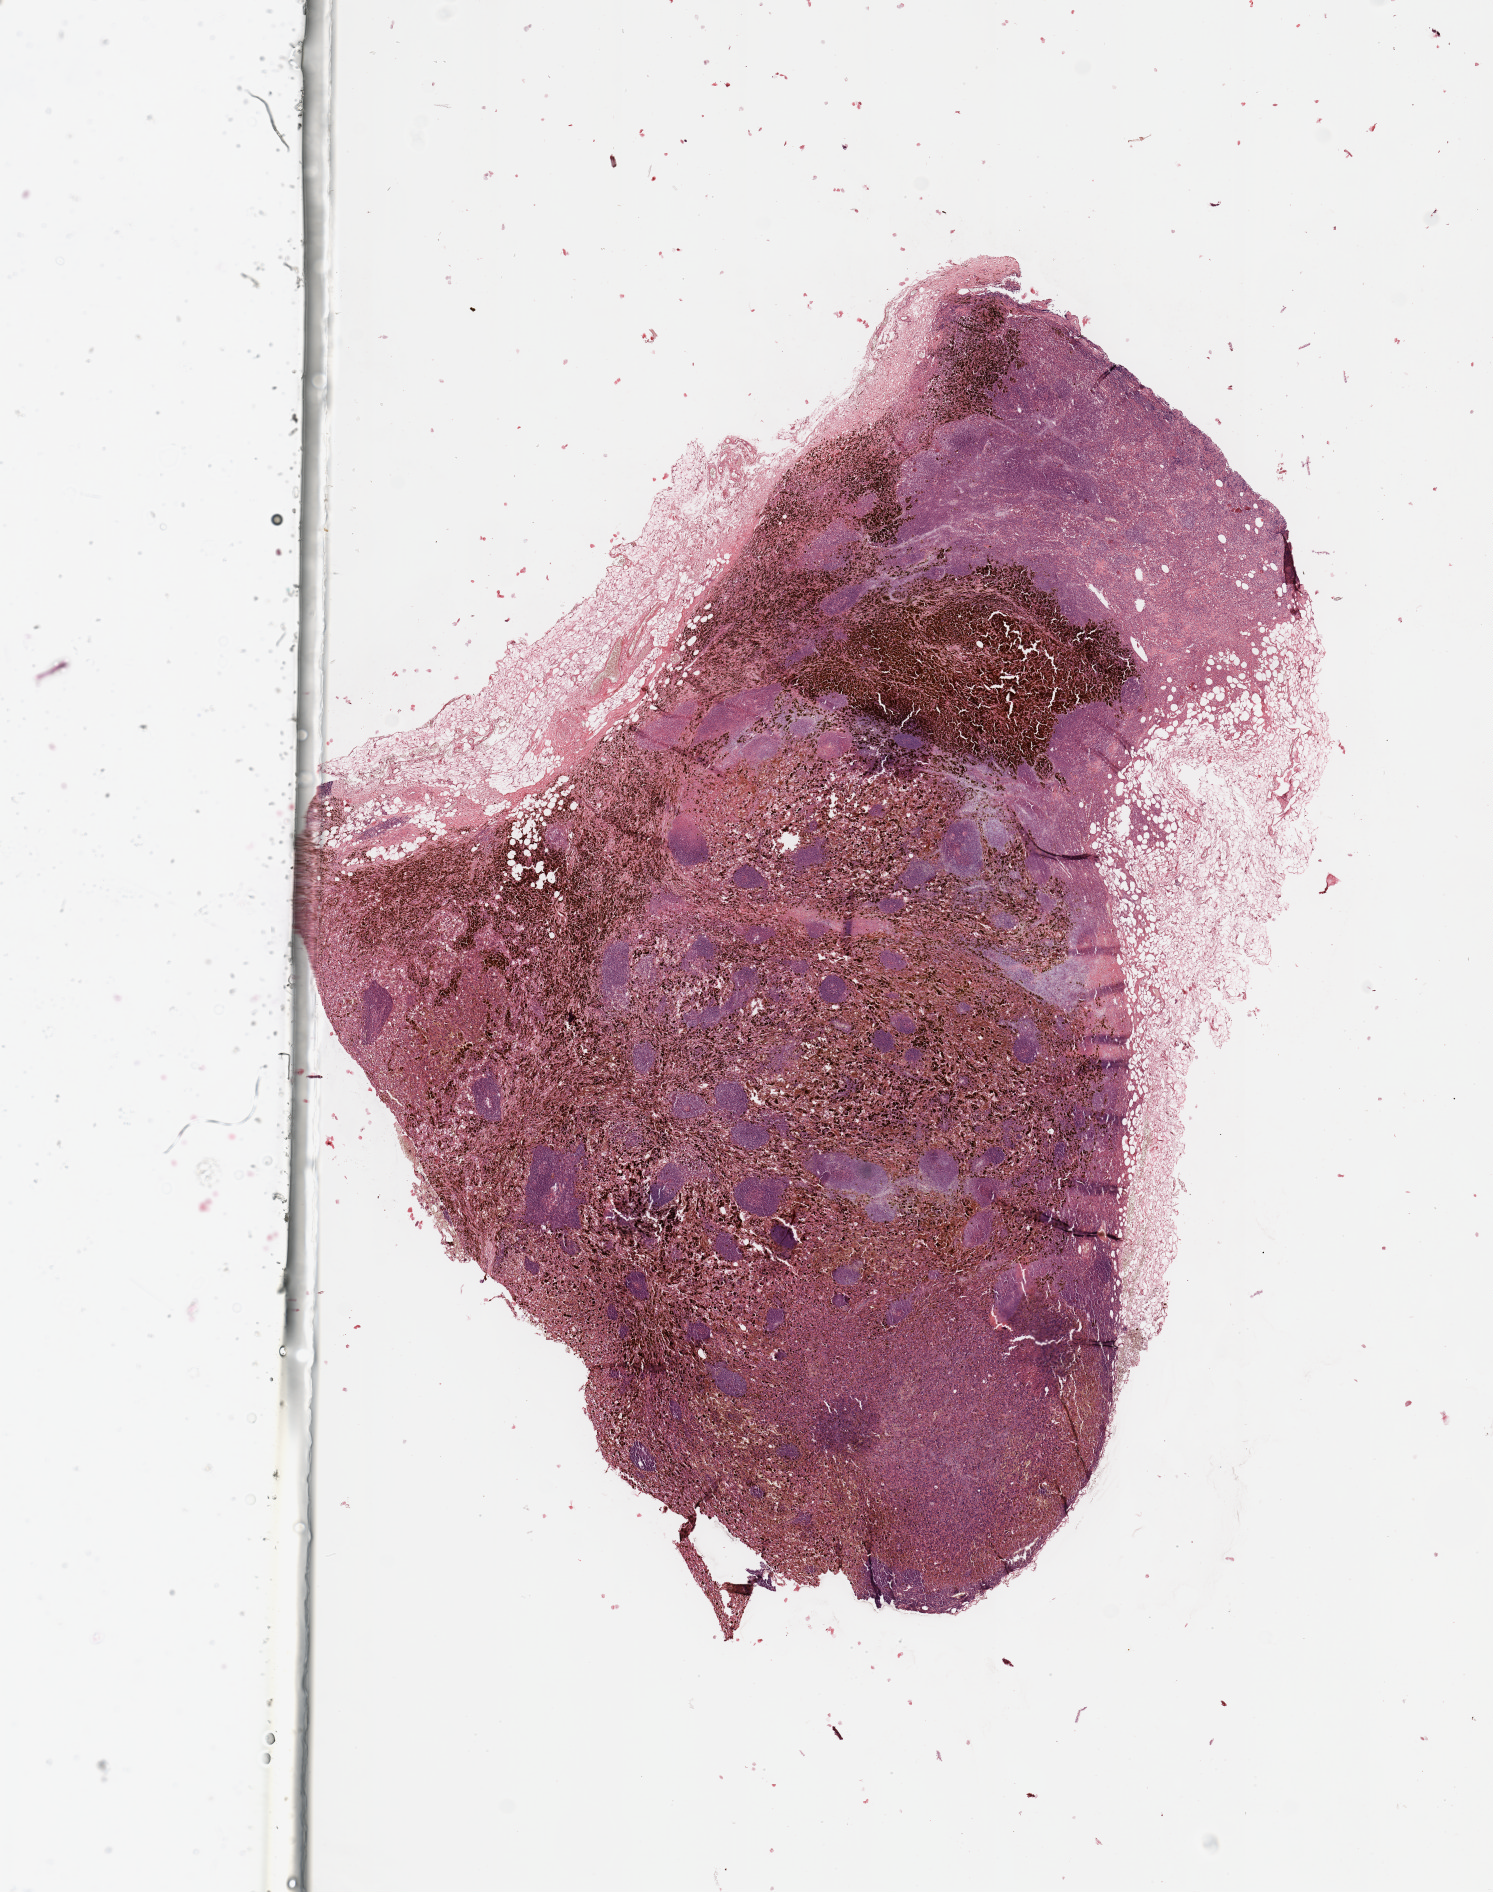
H&E-stained whole-slide image, a low-resolution overview of the entire scanned area, about 11.8 x 15.0 mm. Melanoma tumour tissue; sampled site not recorded. Patient: male, age 74 years.
Primary tumour site (as recorded): palms and soles. Patient diagnosis (cohort enrolment): cutaneous melanoma (skin).